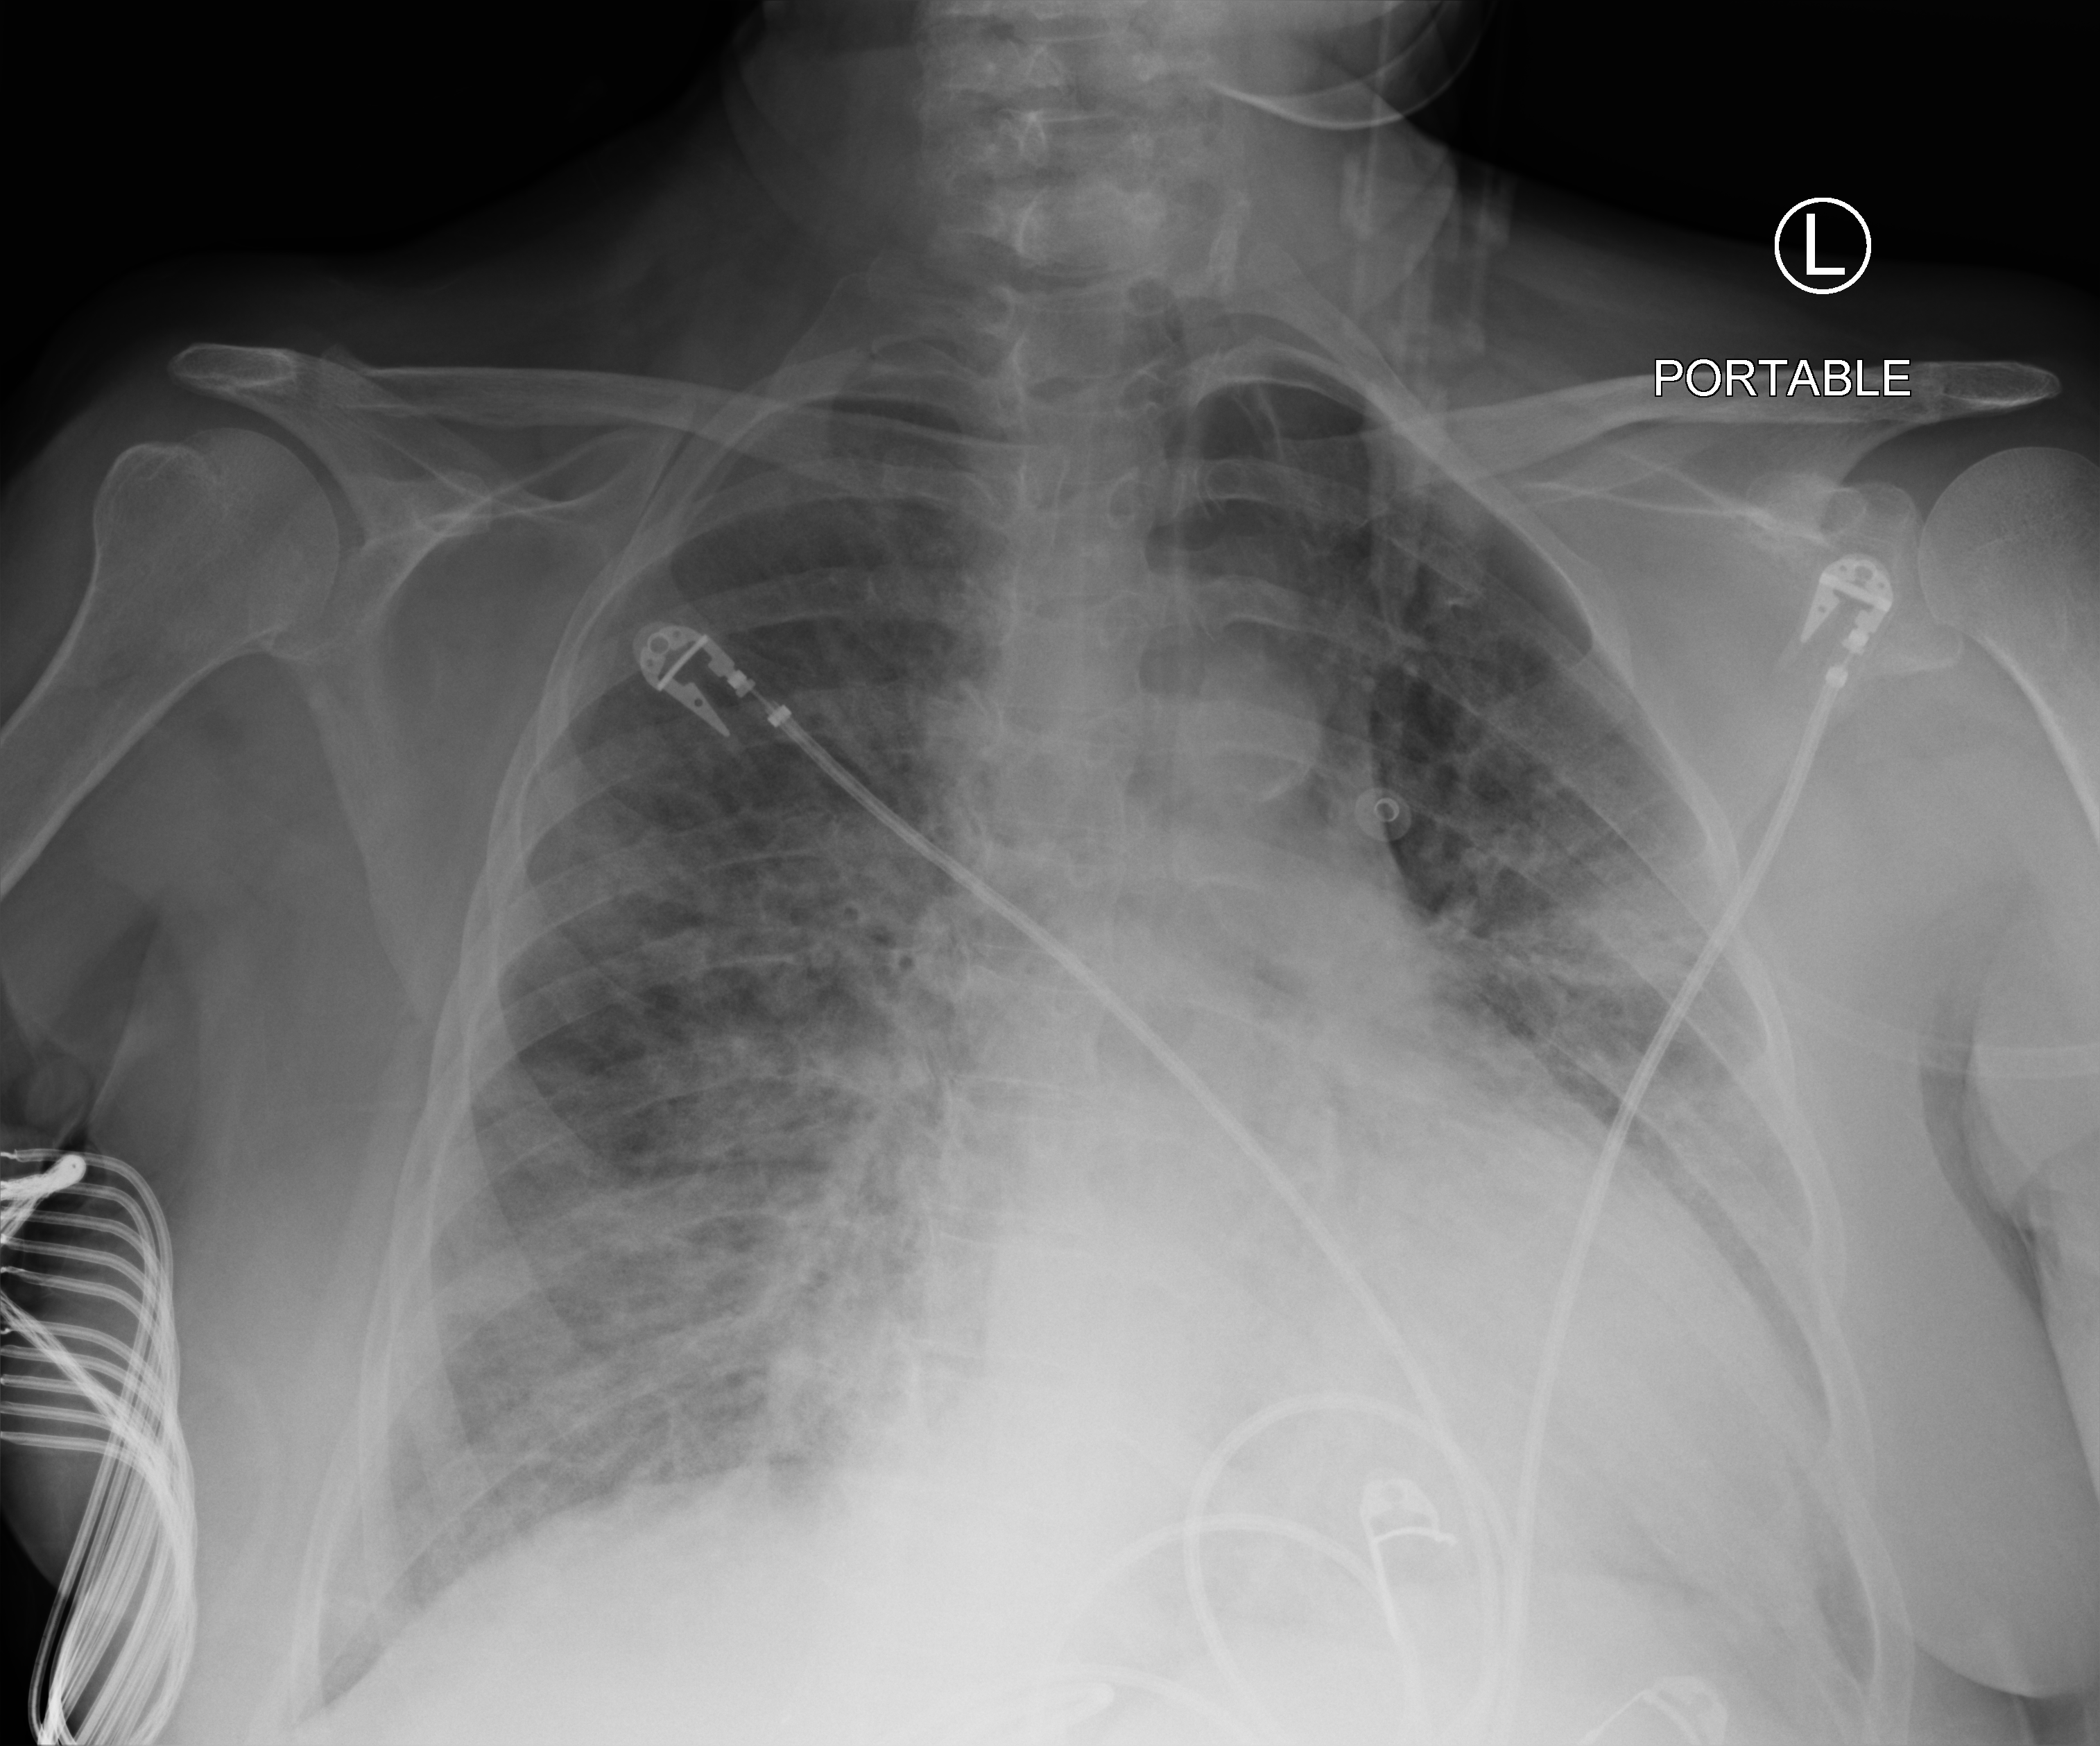
Portable chest radiograph; anteroposterior (AP) projection. Female patient hospitalised with COVID-19, age 60–74 years.
Admission-level facts for this patient (not findings on this image; timing relative to this image not recorded): mechanically ventilated during this hospital stay: no.